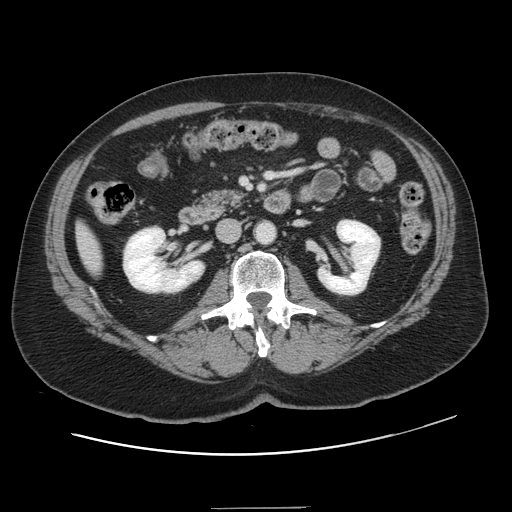
Contrast-enhanced abdominal CT, one axial slice. Position 47 of 143 along the scan axis. 120 kVp. Intravenous contrast given. Soft-tissue window (W 400 / L 40 HU). 512 × 512 image matrix. Male patient, age 62 years. Case-level facts recorded for this patient, not image findings: diagnosis: colorectal cancer liver metastases, imaged before liver resection; multiple liver metastases: yes; largest metastasis: 2.7 cm; chemotherapy before resection: yes.
Annotated regions visible in this slice (manually delineated by an expert):
- liver: box from (x=78, y=227) to (x=101, y=272) px